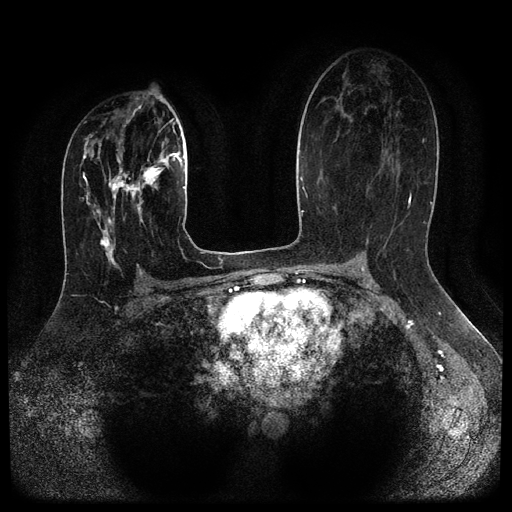
Breast MRI (dynamic contrast-enhanced, multi-phase), one axial slice; slice 59 of 116 in the series (ordered by position); dynamic contrast-enhanced series, time point 2 of 5 at this slice position (early post-contrast); 1.5 T; TE 2.6 ms, TR 5.4 ms; 2 mm slice thickness; 512 × 512 image matrix, field of view 340 × 340 mm. Female patient, age 29 years.
Outlined on this slice (semi-automatically segmented with operator editing):
- breast lesion (labelled 'tumour' in the annotation; benign lesions carry a separate 'benign' label): bounding box (x1, y1, x2, y2) in pixels: (109, 151, 170, 204)
- breast lesion (labelled benign in the annotation): (92, 209, 122, 275)